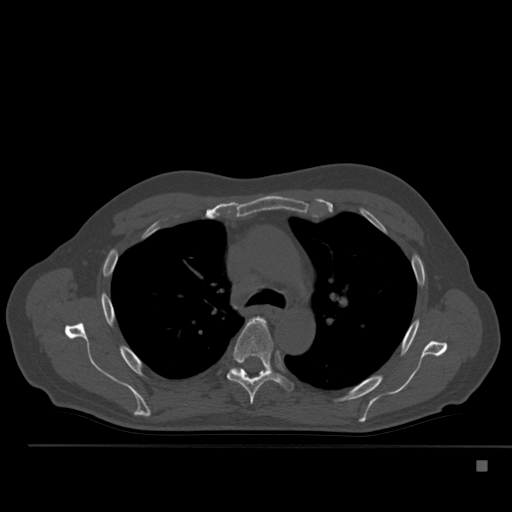
CT including the spine, one axial slice. Slice 365 of 517 in the series (ordered by position). Reconstruction kernel Br40s. 120 kVp. Bone window (W 1800 / L 400 HU). 1.5 mm slice thickness. 512 × 512 image matrix, field of view 408 × 408 mm. Male patient, age 70 years. From the clinical record (not read from this slice): primary cancer: renal; vertebrae with lytic lesions (as recorded): T4, T6, T10, T12, L3, L4, L5.
Outlined on this slice (semi-automatically segmented with operator editing):
- T5 vertebra: bounding box <227,317,293,405> (left, top, right, bottom; pixels)
- T6 vertebra: <234,368,240,370>